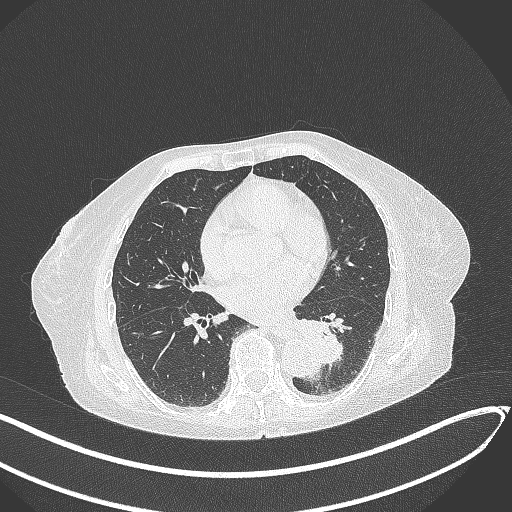
Chest CT, one axial slice. Position 110 of 324 along the scan axis. Reconstruction kernel B70f. Lung window (W 1500 / L -600 HU). 512 × 512 image matrix. Female patient, age 82 years. Case-level facts recorded for this patient, not image findings: clinical TNM (as recorded): T1b N0 M1.
Annotated regions visible in this slice (rectangle marked by the reading radiologist):
- lung tumour (recorded histology: adenocarcinoma): box from (x=292, y=314) to (x=346, y=369) px